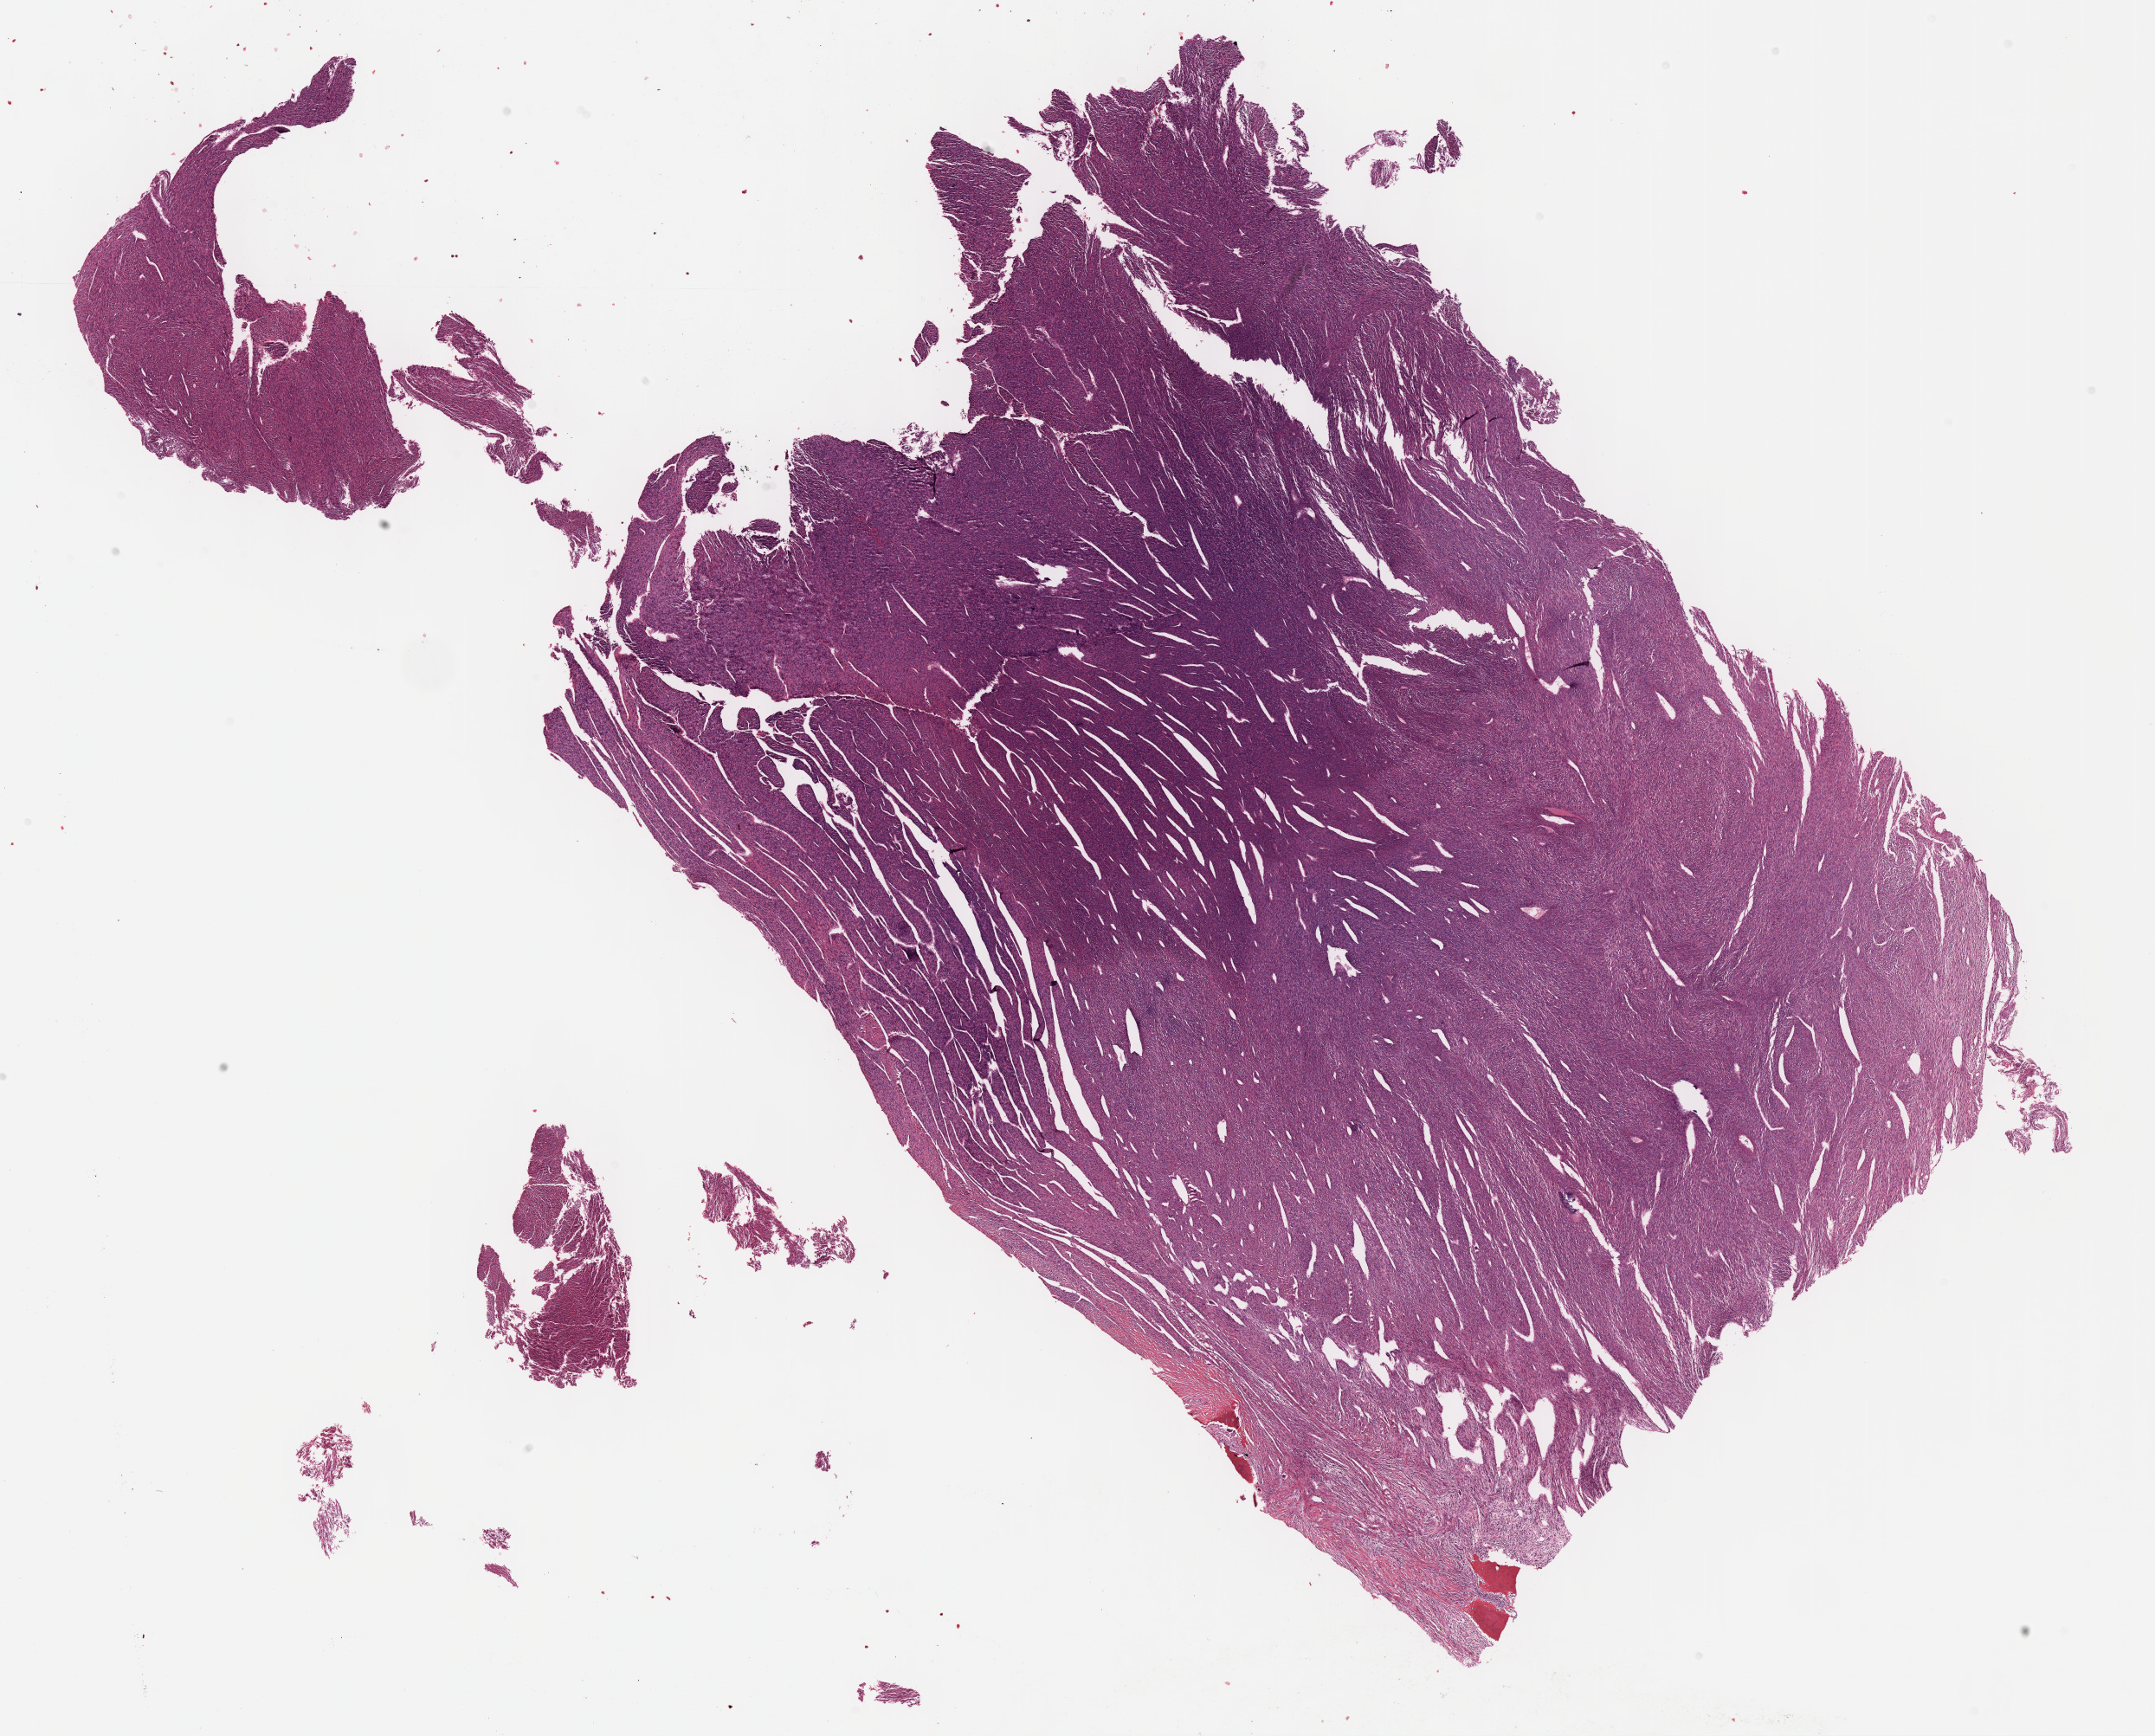
H&E-stained whole-slide image — whole scanned area (about 20.1 x 16.2 mm) shown as a low-resolution overview; FFPE section; sample: primary tumour, bones, joints and articular cartilage of limbs. Female, age 47 years at initial diagnosis.
Histologic diagnosis: Leiomyosarcoma, NOS (short bones of lower limb and associated joints).